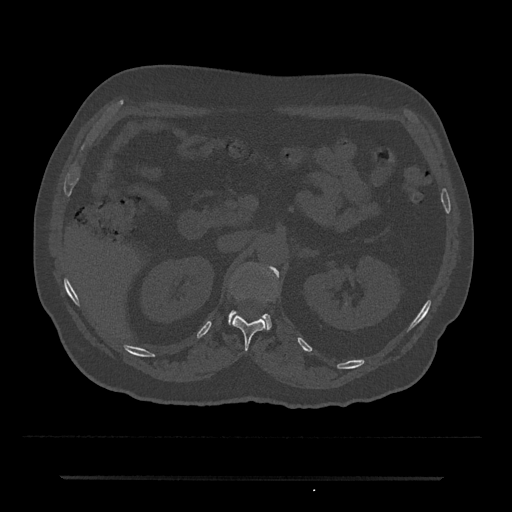
CT including the spine, one axial slice; position 109 of 797 along the scan axis; bone window (W 1800 / L 400 HU); 0.5 mm slice thickness; 512 × 512 image matrix, field of view 437 × 437 mm. Patient: male, 69 years. From the clinical record (not read from this slice): primary cancer: prostate.
Outlined on this slice (semi-automatic segmentation, software-assisted and operator-edited):
- L1 vertebra: box from (x=229, y=266) to (x=279, y=328) px
- T12 vertebra: (x=229, y=290)–(x=267, y=349)